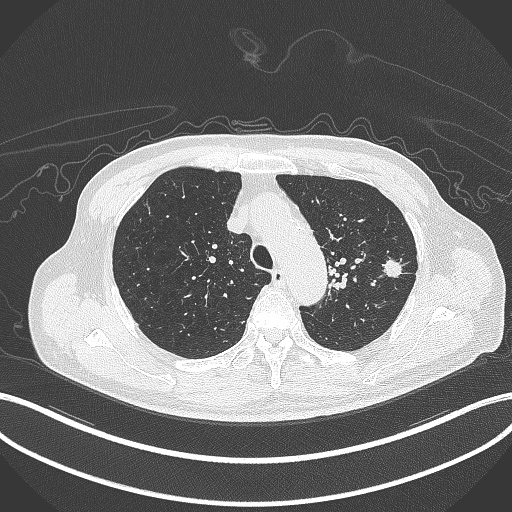
Chest CT, one axial slice. Slice 336 of 417 in the series (ordered by position). 120 kVp. Lung window (W 1500 / L -600 HU). 1 mm slice thickness. 512 × 512 image matrix, field of view 400 × 400 mm. Patient: male, 77 years. From the clinical record (not read from this slice): clinical TNM (as recorded): T3 N1 M0.
Outlined on this slice (bounding box drawn by a radiologist):
- lung tumour (recorded histology: adenocarcinoma): bounding box <378,256,404,280> (left, top, right, bottom; pixels)